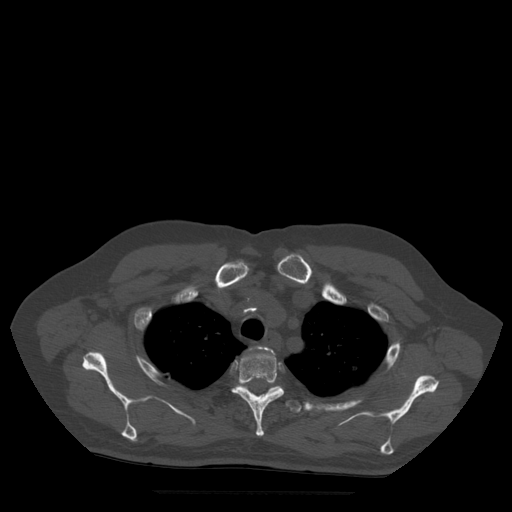
CT including the spine, one axial slice; bone window (W 1800 / L 400 HU); 1.25 mm slice thickness; 512 × 512 image matrix. Patient age 72 years. From the clinical record (not read from this slice): primary cancer: prostate.
Structures marked on this image (semi-automatic segmentation, software-assisted and operator-edited):
- T2 vertebra: bounding box [x1, y1, x2, y2] px = [250, 347, 275, 354]
- T3 vertebra: [232, 348, 284, 437]
- T4 vertebra: [238, 383, 302, 413]